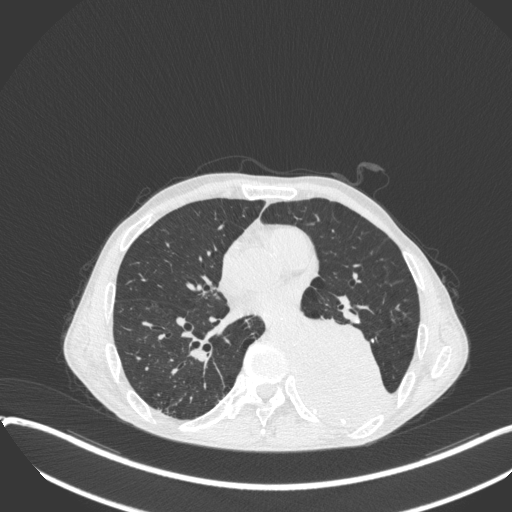
Chest CT, one axial slice; position 168 of 400 along the scan axis; 120 kVp; lung window (W 1500 / L -600 HU); 512 × 512 image matrix. Patient: male, 57 years. Case-level facts recorded for this patient, not image findings: clinical TNM (as recorded): T4 N0 M0.
Outlined on this slice (rectangle marked by the reading radiologist):
- lung tumour (recorded histology: squamous cell carcinoma): bounding box [x1, y1, x2, y2] px = [300, 312, 396, 423]